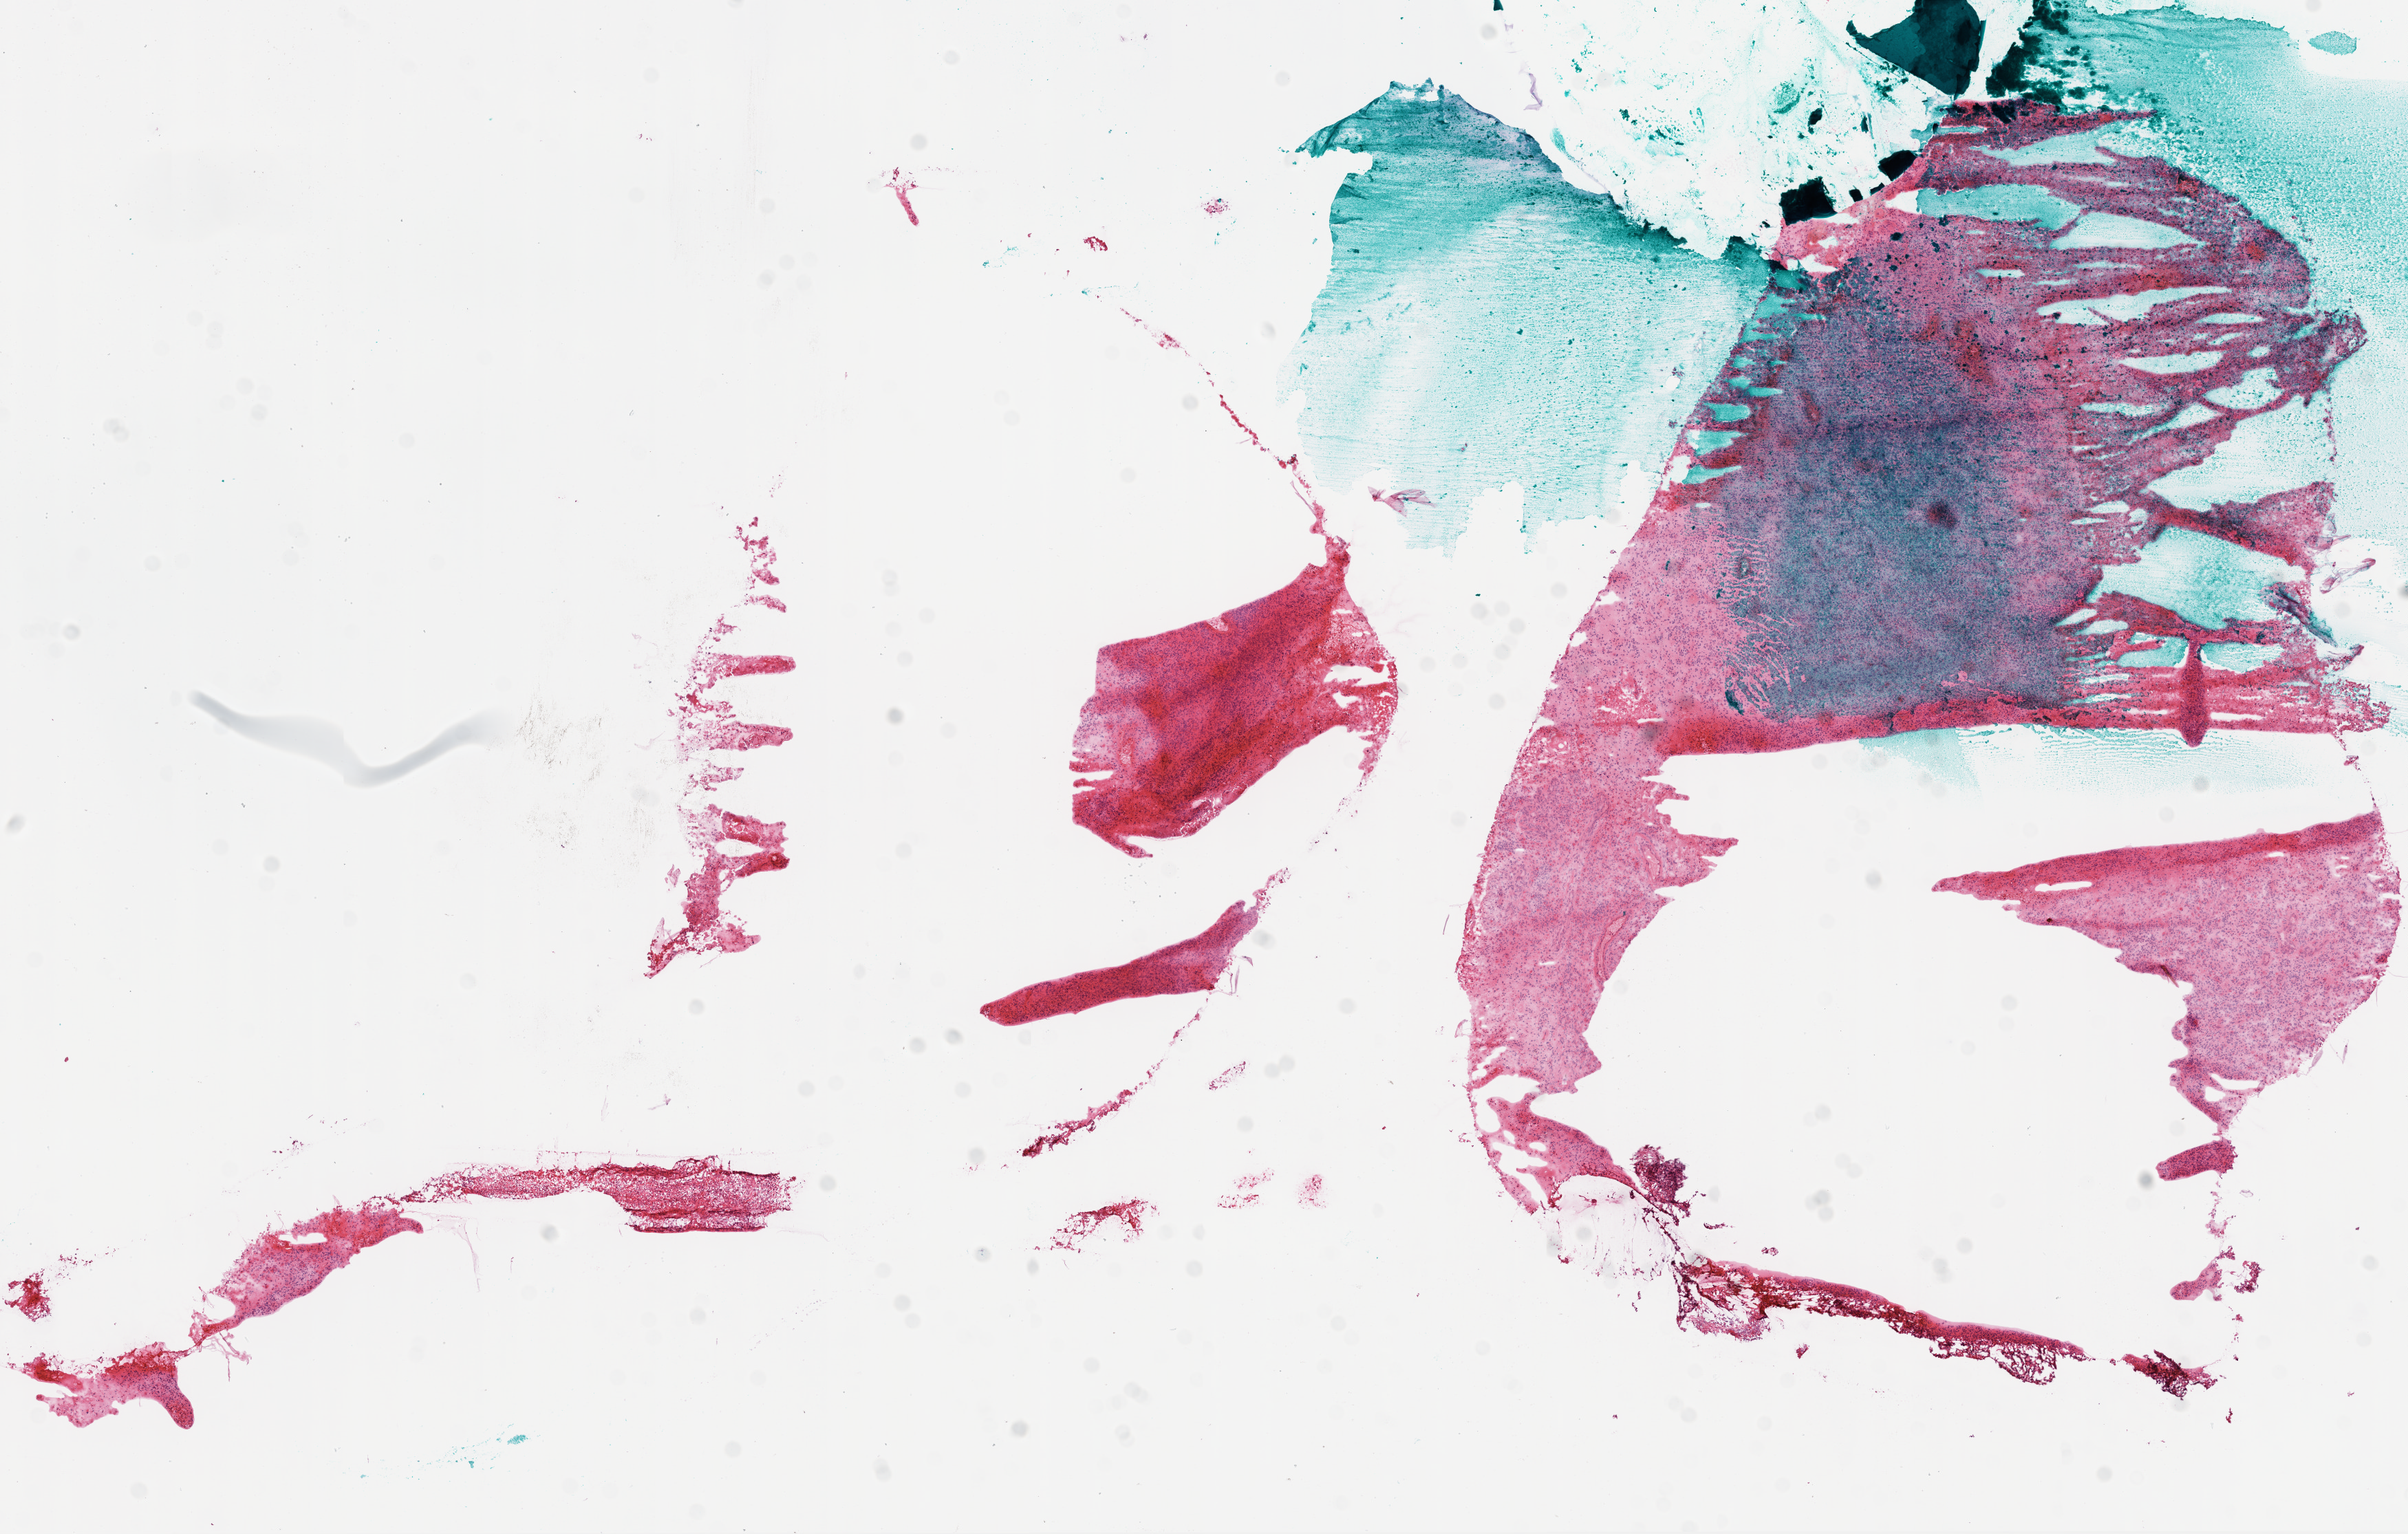
Digitized Hematoxylin and eosin (H&E) stained tissue section (whole slide) — whole scanned area (about 14.0 x 8.9 mm, acquisition: 20x scan) shown as a low-resolution overview, frozen section, brain, primary tumour sample. Male, age 39 years at initial diagnosis. Pathologist review of this section (percent, as recorded): tumour cells 80%, tumour nuclei 100%, normal cells 0%, stromal cells 0%, necrosis 20%.
Pathologic diagnosis: Glioblastoma.